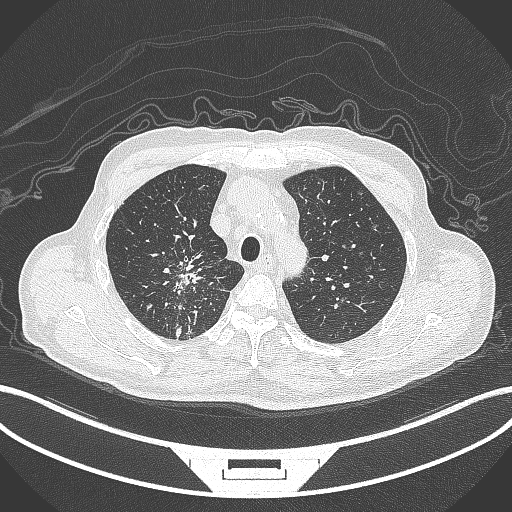
Chest CT, one axial slice; position 295 of 407 along the scan axis; lung window (W 1500 / L -600 HU); 512 × 512 image matrix. Patient: male, 69 years. Case-level facts recorded for this patient, not image findings: clinical TNM (as recorded): T1c N1 M1.
Outlined on this slice (rectangle marked by the reading radiologist):
- lung tumour (recorded histology: adenocarcinoma): box from (x=170, y=252) to (x=214, y=305) px